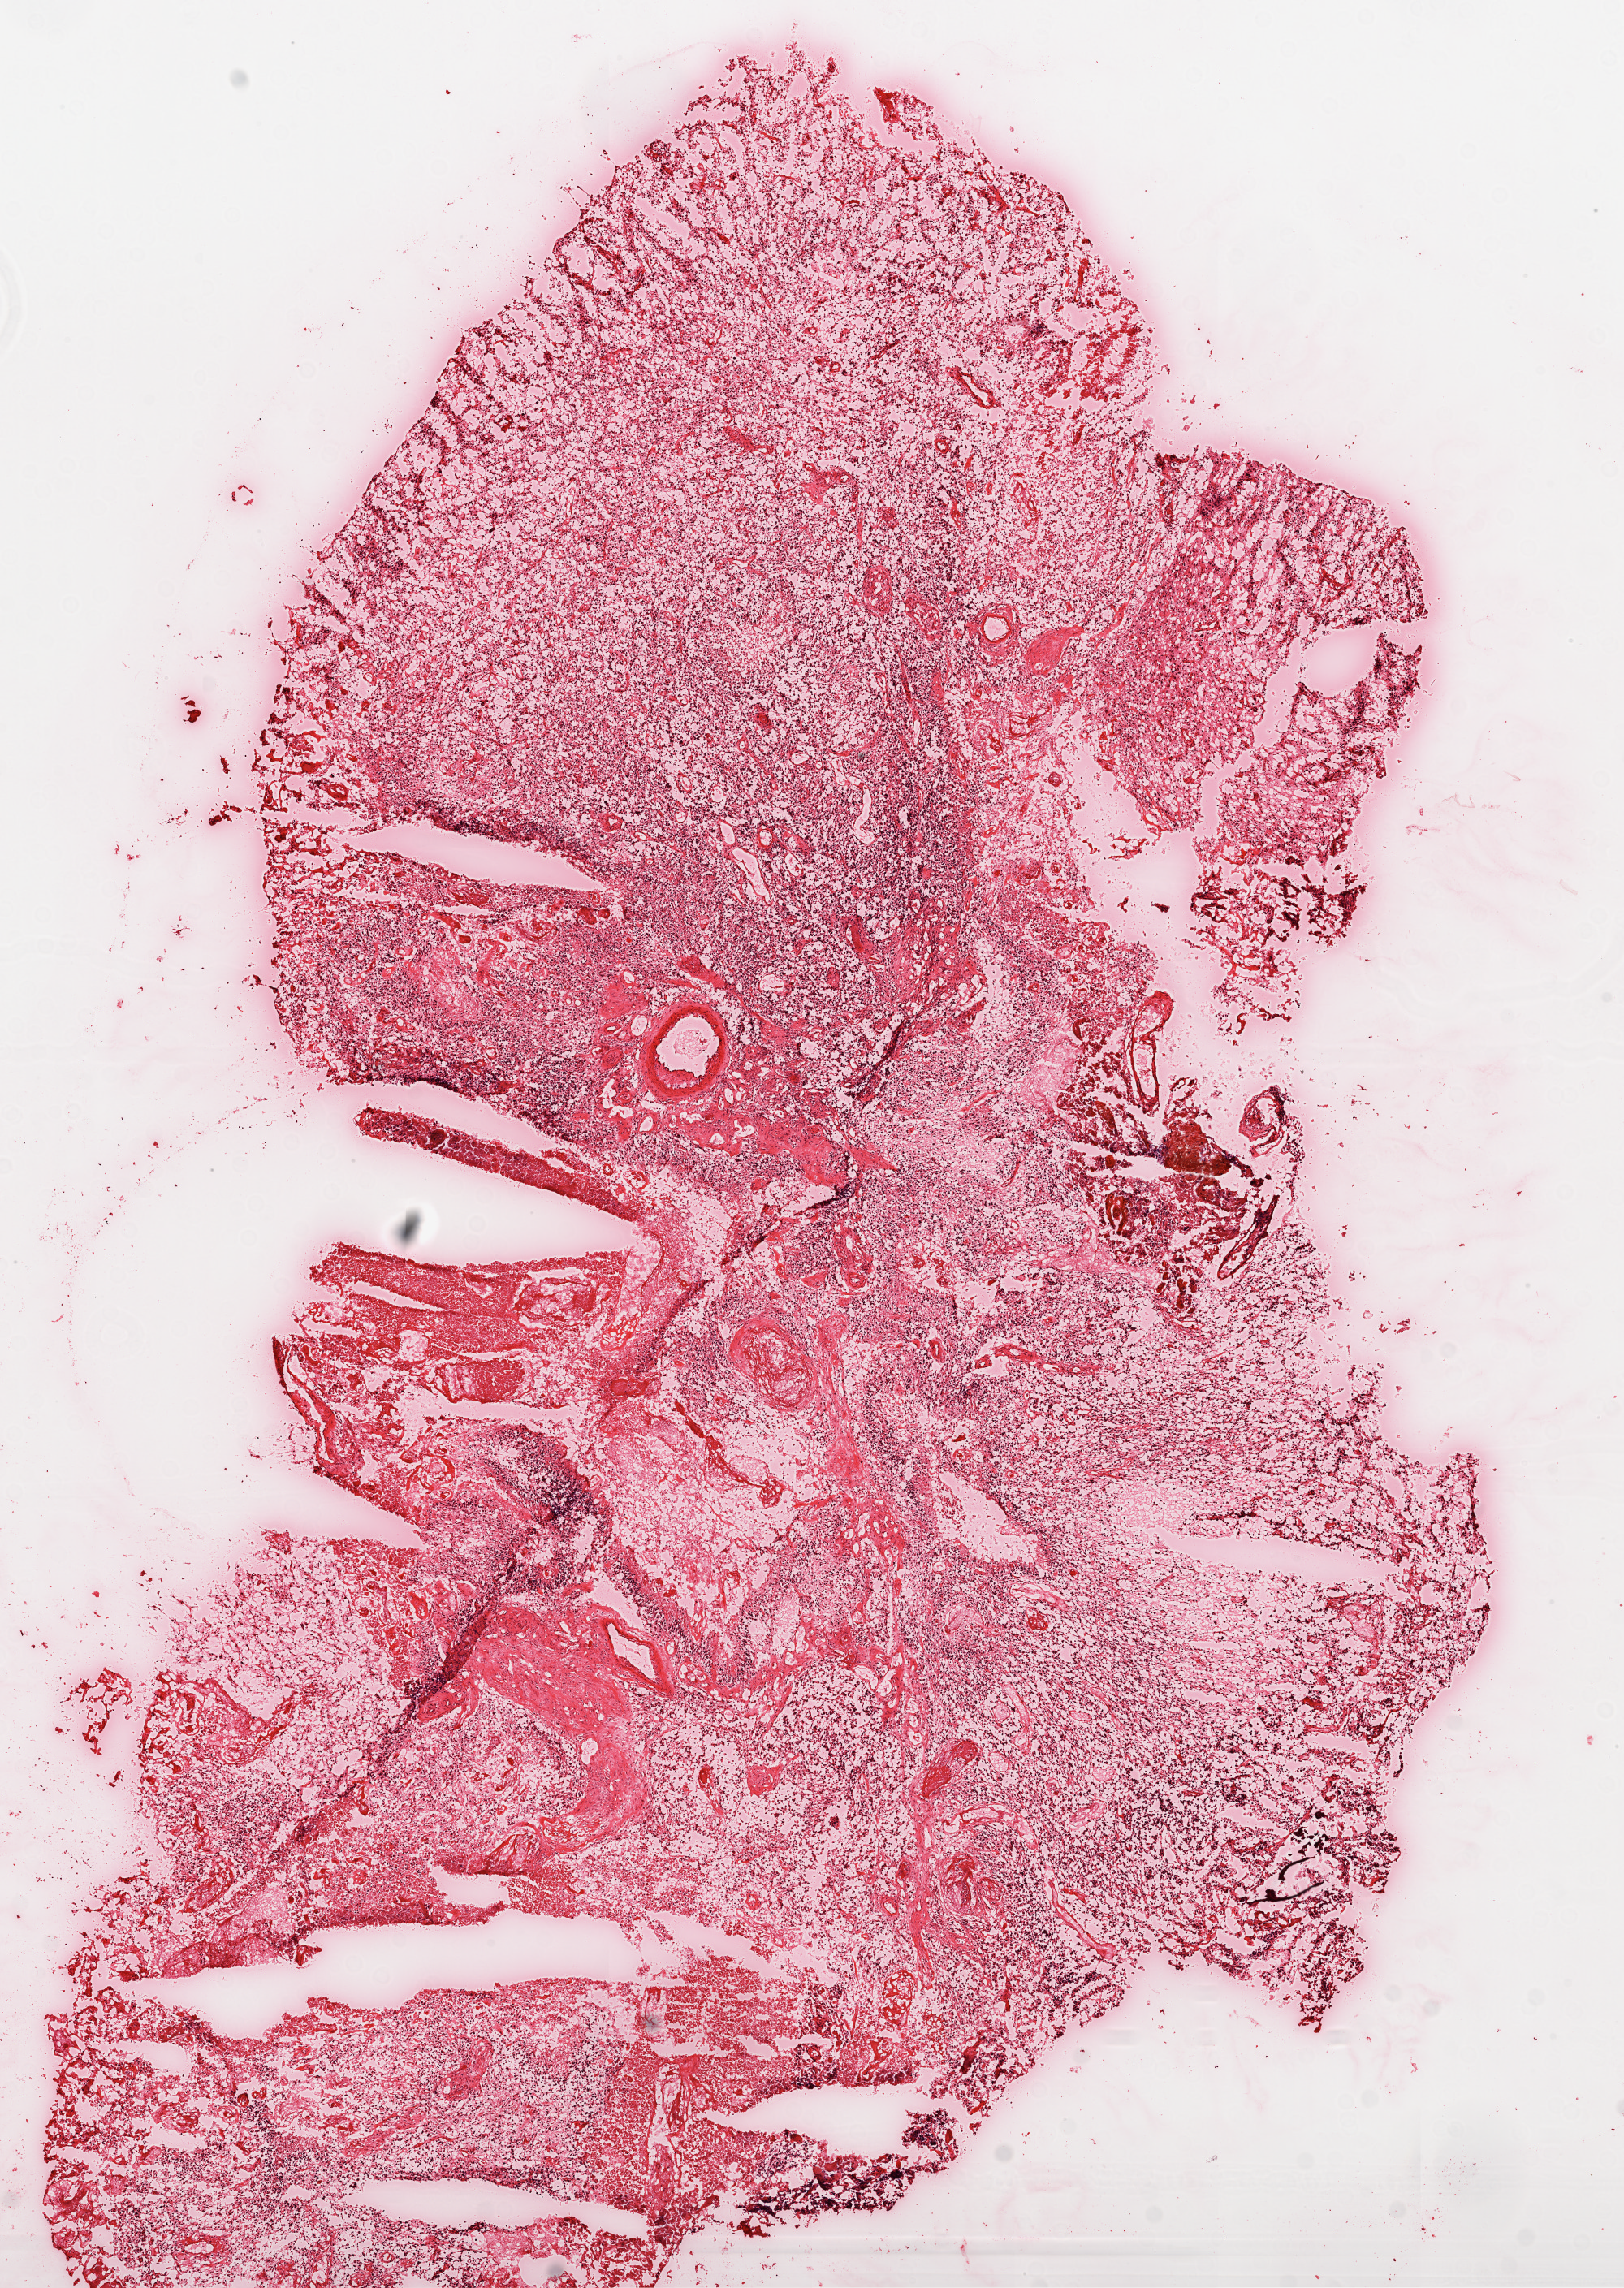
Whole-slide histology image, Hematoxylin and eosin (H&E) stained, whole scanned area (about 8.0 x 11.3 mm, acquisition: 20x scan) shown as a low-resolution overview. Frozen section from the top of the tissue portion. Primary tumour sample from the brain. Female patient; age at initial diagnosis 36 years. Composition of this section per pathologist review: tumour cells 80%, tumour nuclei 95%, normal cells 0%, stromal cells 10%, necrosis 10%.
Histologic diagnosis: Glioblastoma.